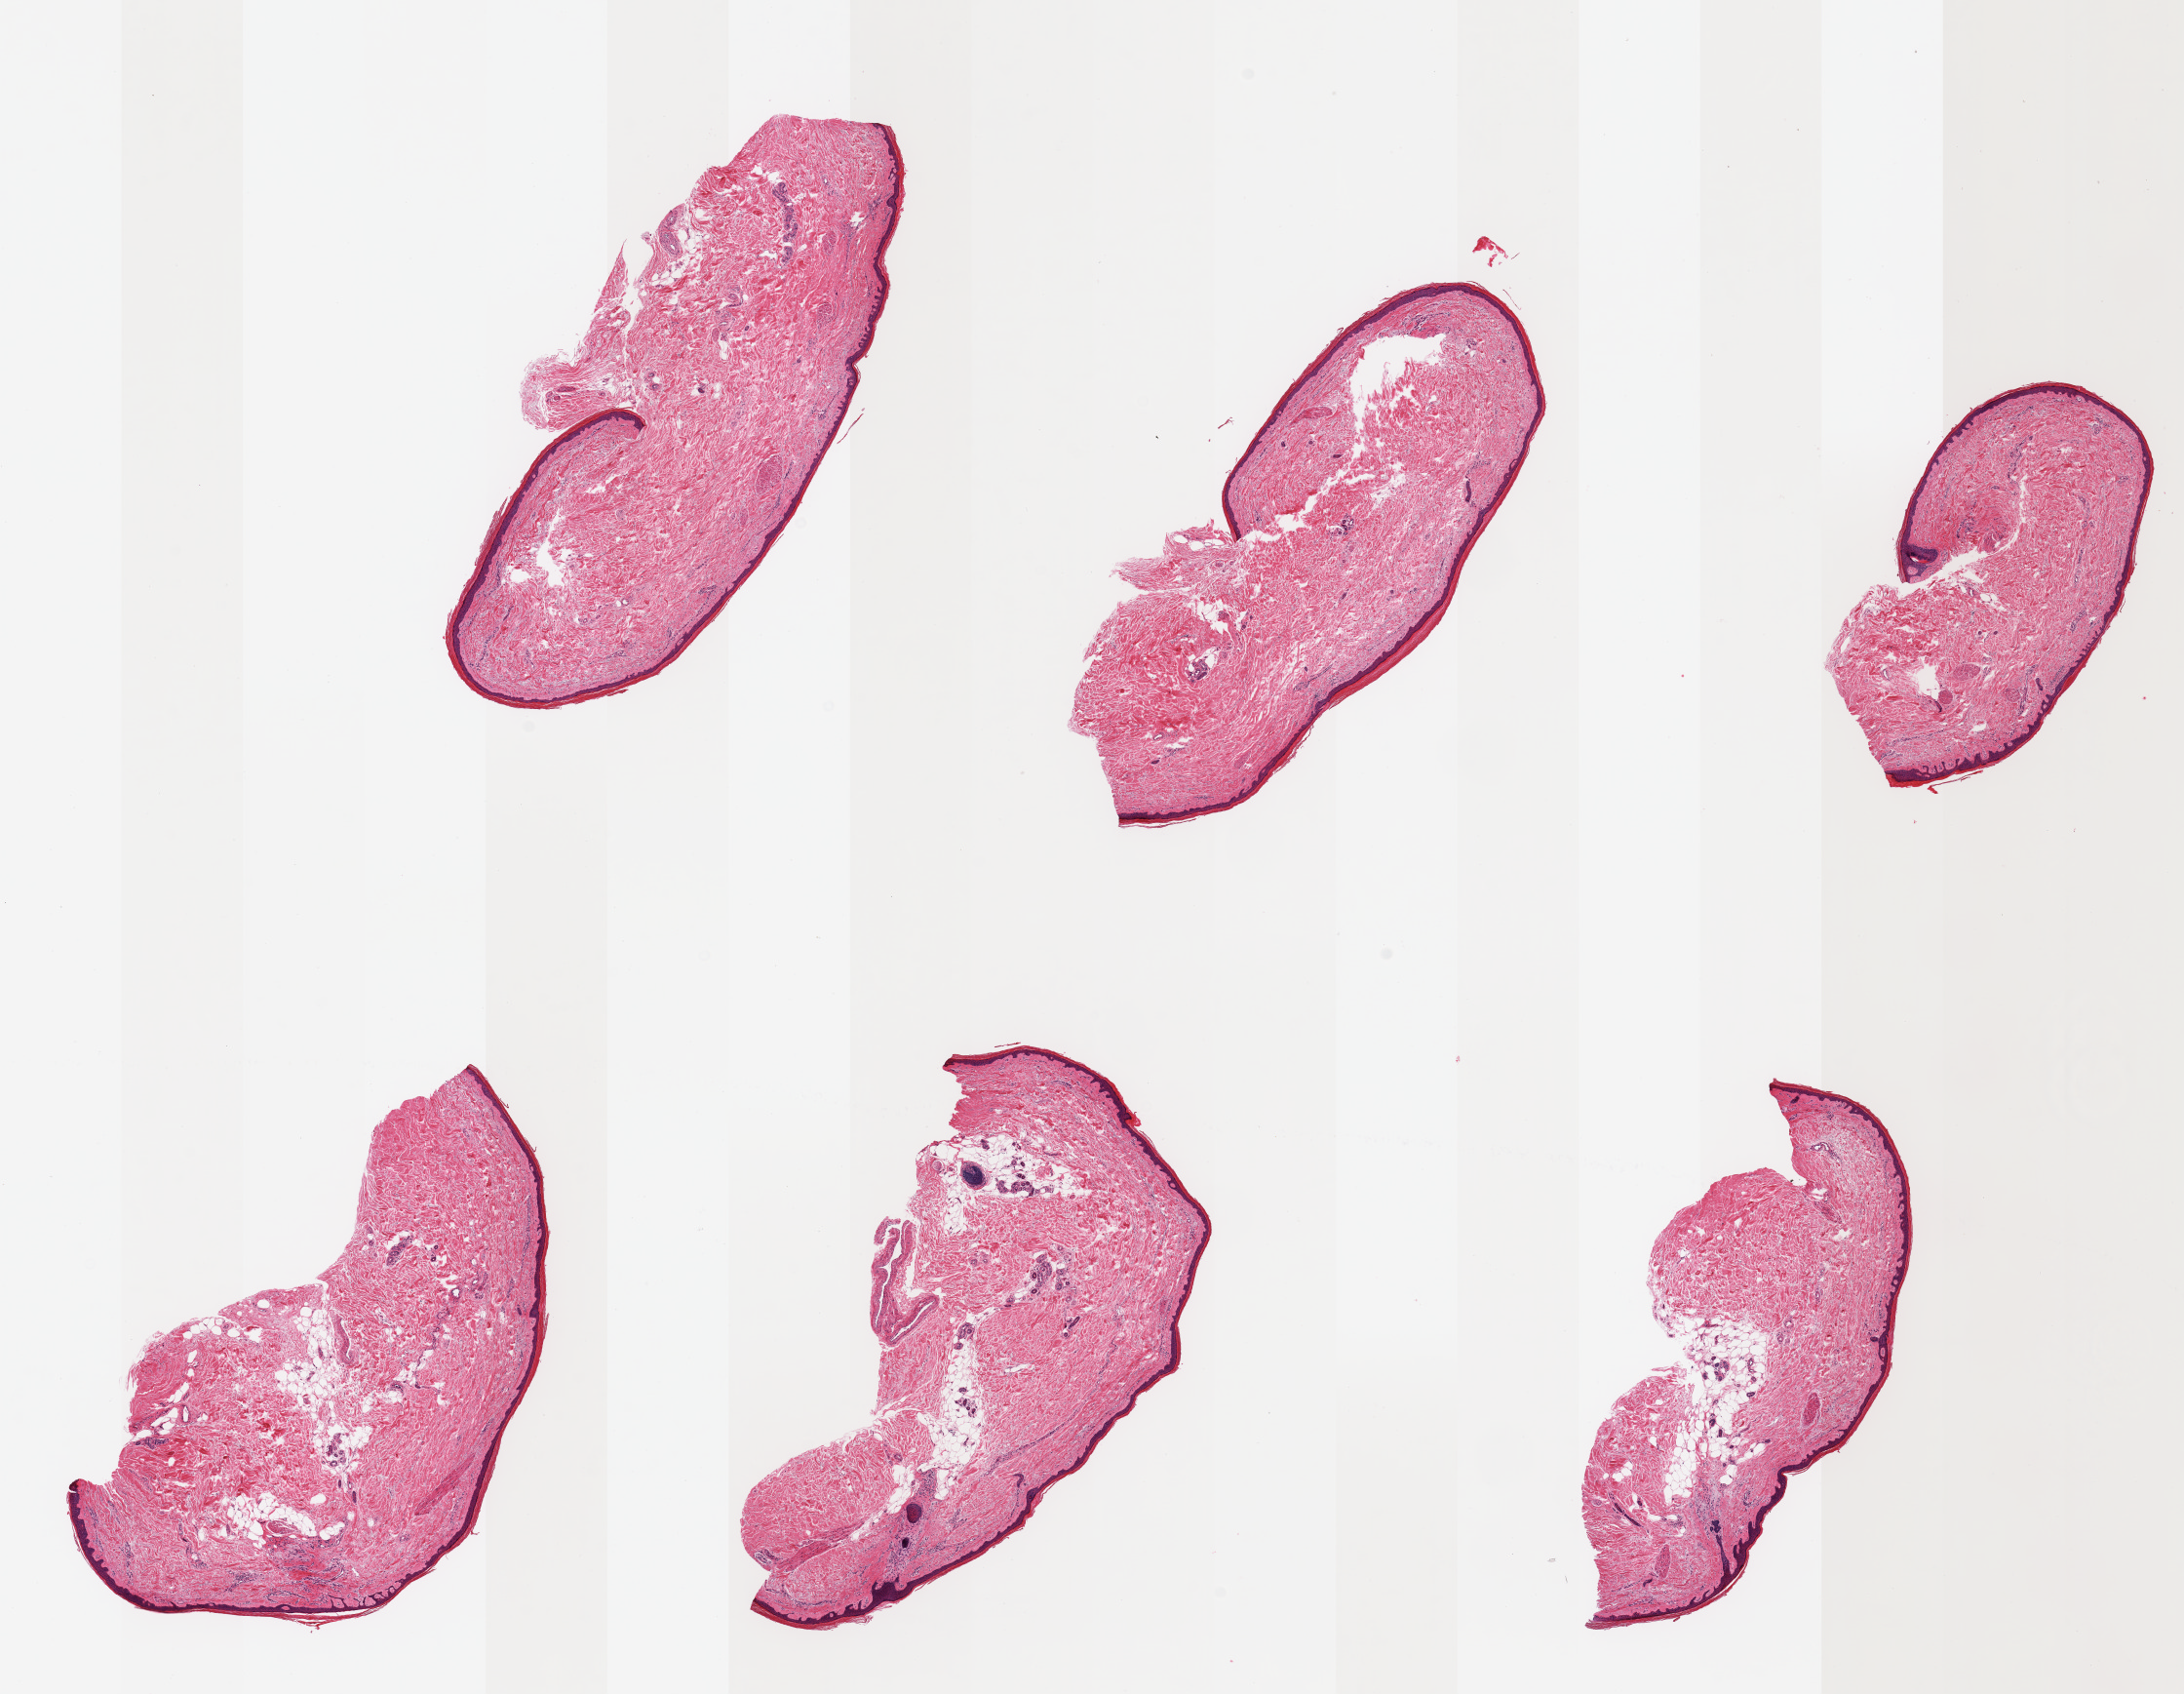
Whole-slide image, haematoxylin and eosin stain, brightfield, whole scanned area (about 17.7 x 13.7 mm, from a 20x scan) shown as a low-resolution overview, PAXgene-fixed, paraffin-embedded tissue, target tissue: skin of lower leg, donor tissue sample. Donor: female.
- pathologist's review note for this sample: 6 pieces; well trimmed; up to 20% dermal fat